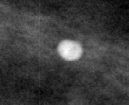
Region of interest cut from a scanned film mammogram (one marked finding), left breast, MLO view, BI-RADS breast density category 1 (scale 1–4).
Finding: calcifications, morphology lucent center; BI-RADS assessment category 2; subtlety rating 5 on a 1 (subtle) to 5 (obvious) scale; benign without callback (not worked up further).